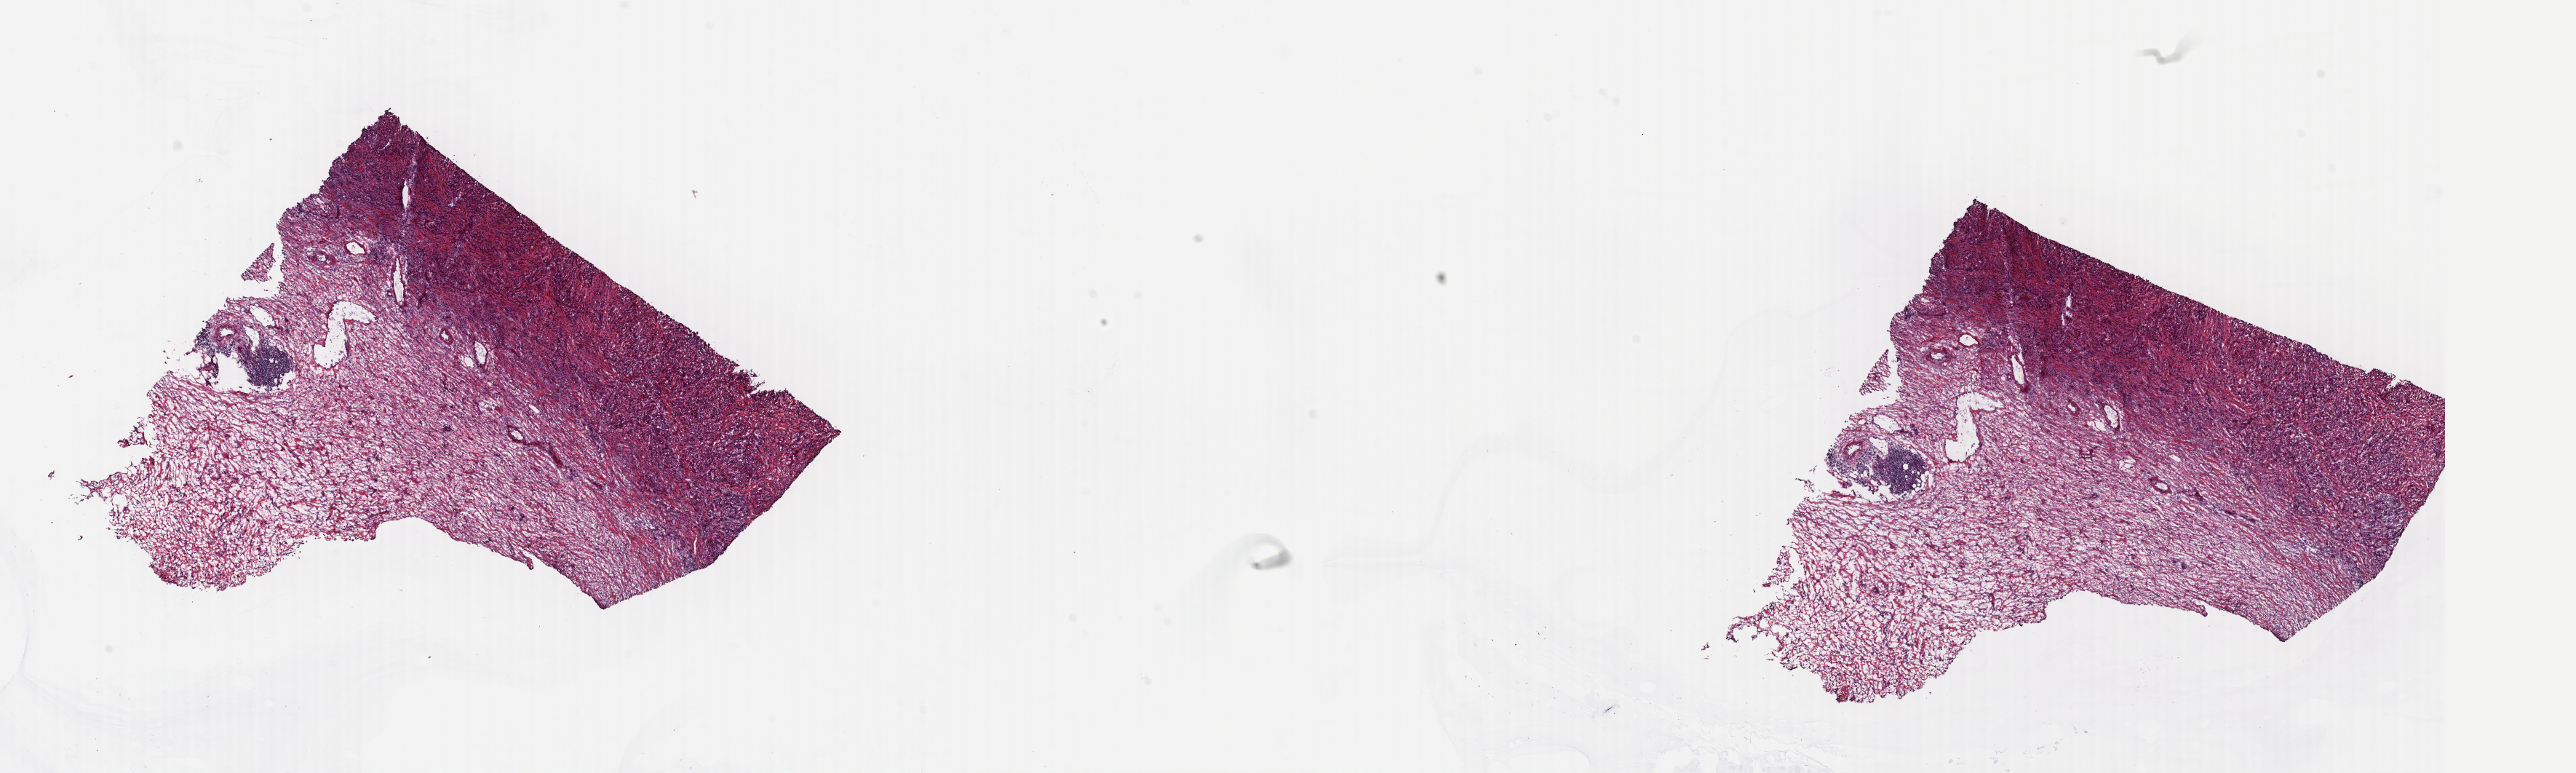
Whole-slide histology image, H&E-stained, low-resolution overview of the scanned area, about 27.8 x 8.3 mm, frozen section from the top of the tissue portion, bladder, primary tumour sample. Male, age 84 years at initial diagnosis.
Pathologic diagnosis: Transitional cell carcinoma (lateral wall of bladder).